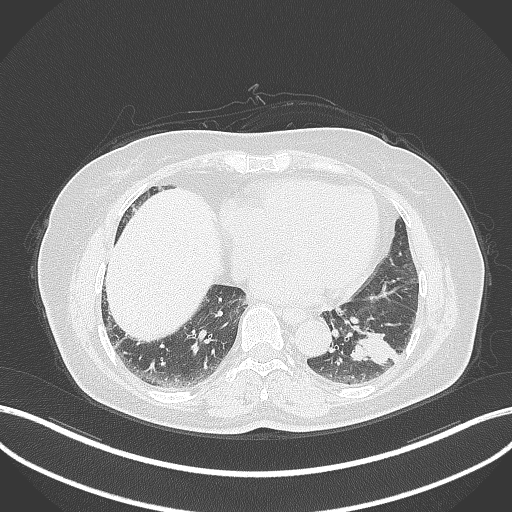
Chest CT, one axial slice. Slice 131 of 311 in the series (ordered by position). 120 kVp. Lung window (W 1500 / L -600 HU). 1 mm slice thickness. 512 × 512 image matrix, field of view 400 × 400 mm. Female patient, age 59 years. Case-level facts recorded for this patient, not image findings: clinical TNM (as recorded): T2a N0 M0; histopathological grade: G2-3.
Structures marked on this image (bounding box drawn by a radiologist):
- lung tumour (recorded histology: adenocarcinoma): bounding box (x1, y1, x2, y2) in pixels: (344, 327, 396, 371)